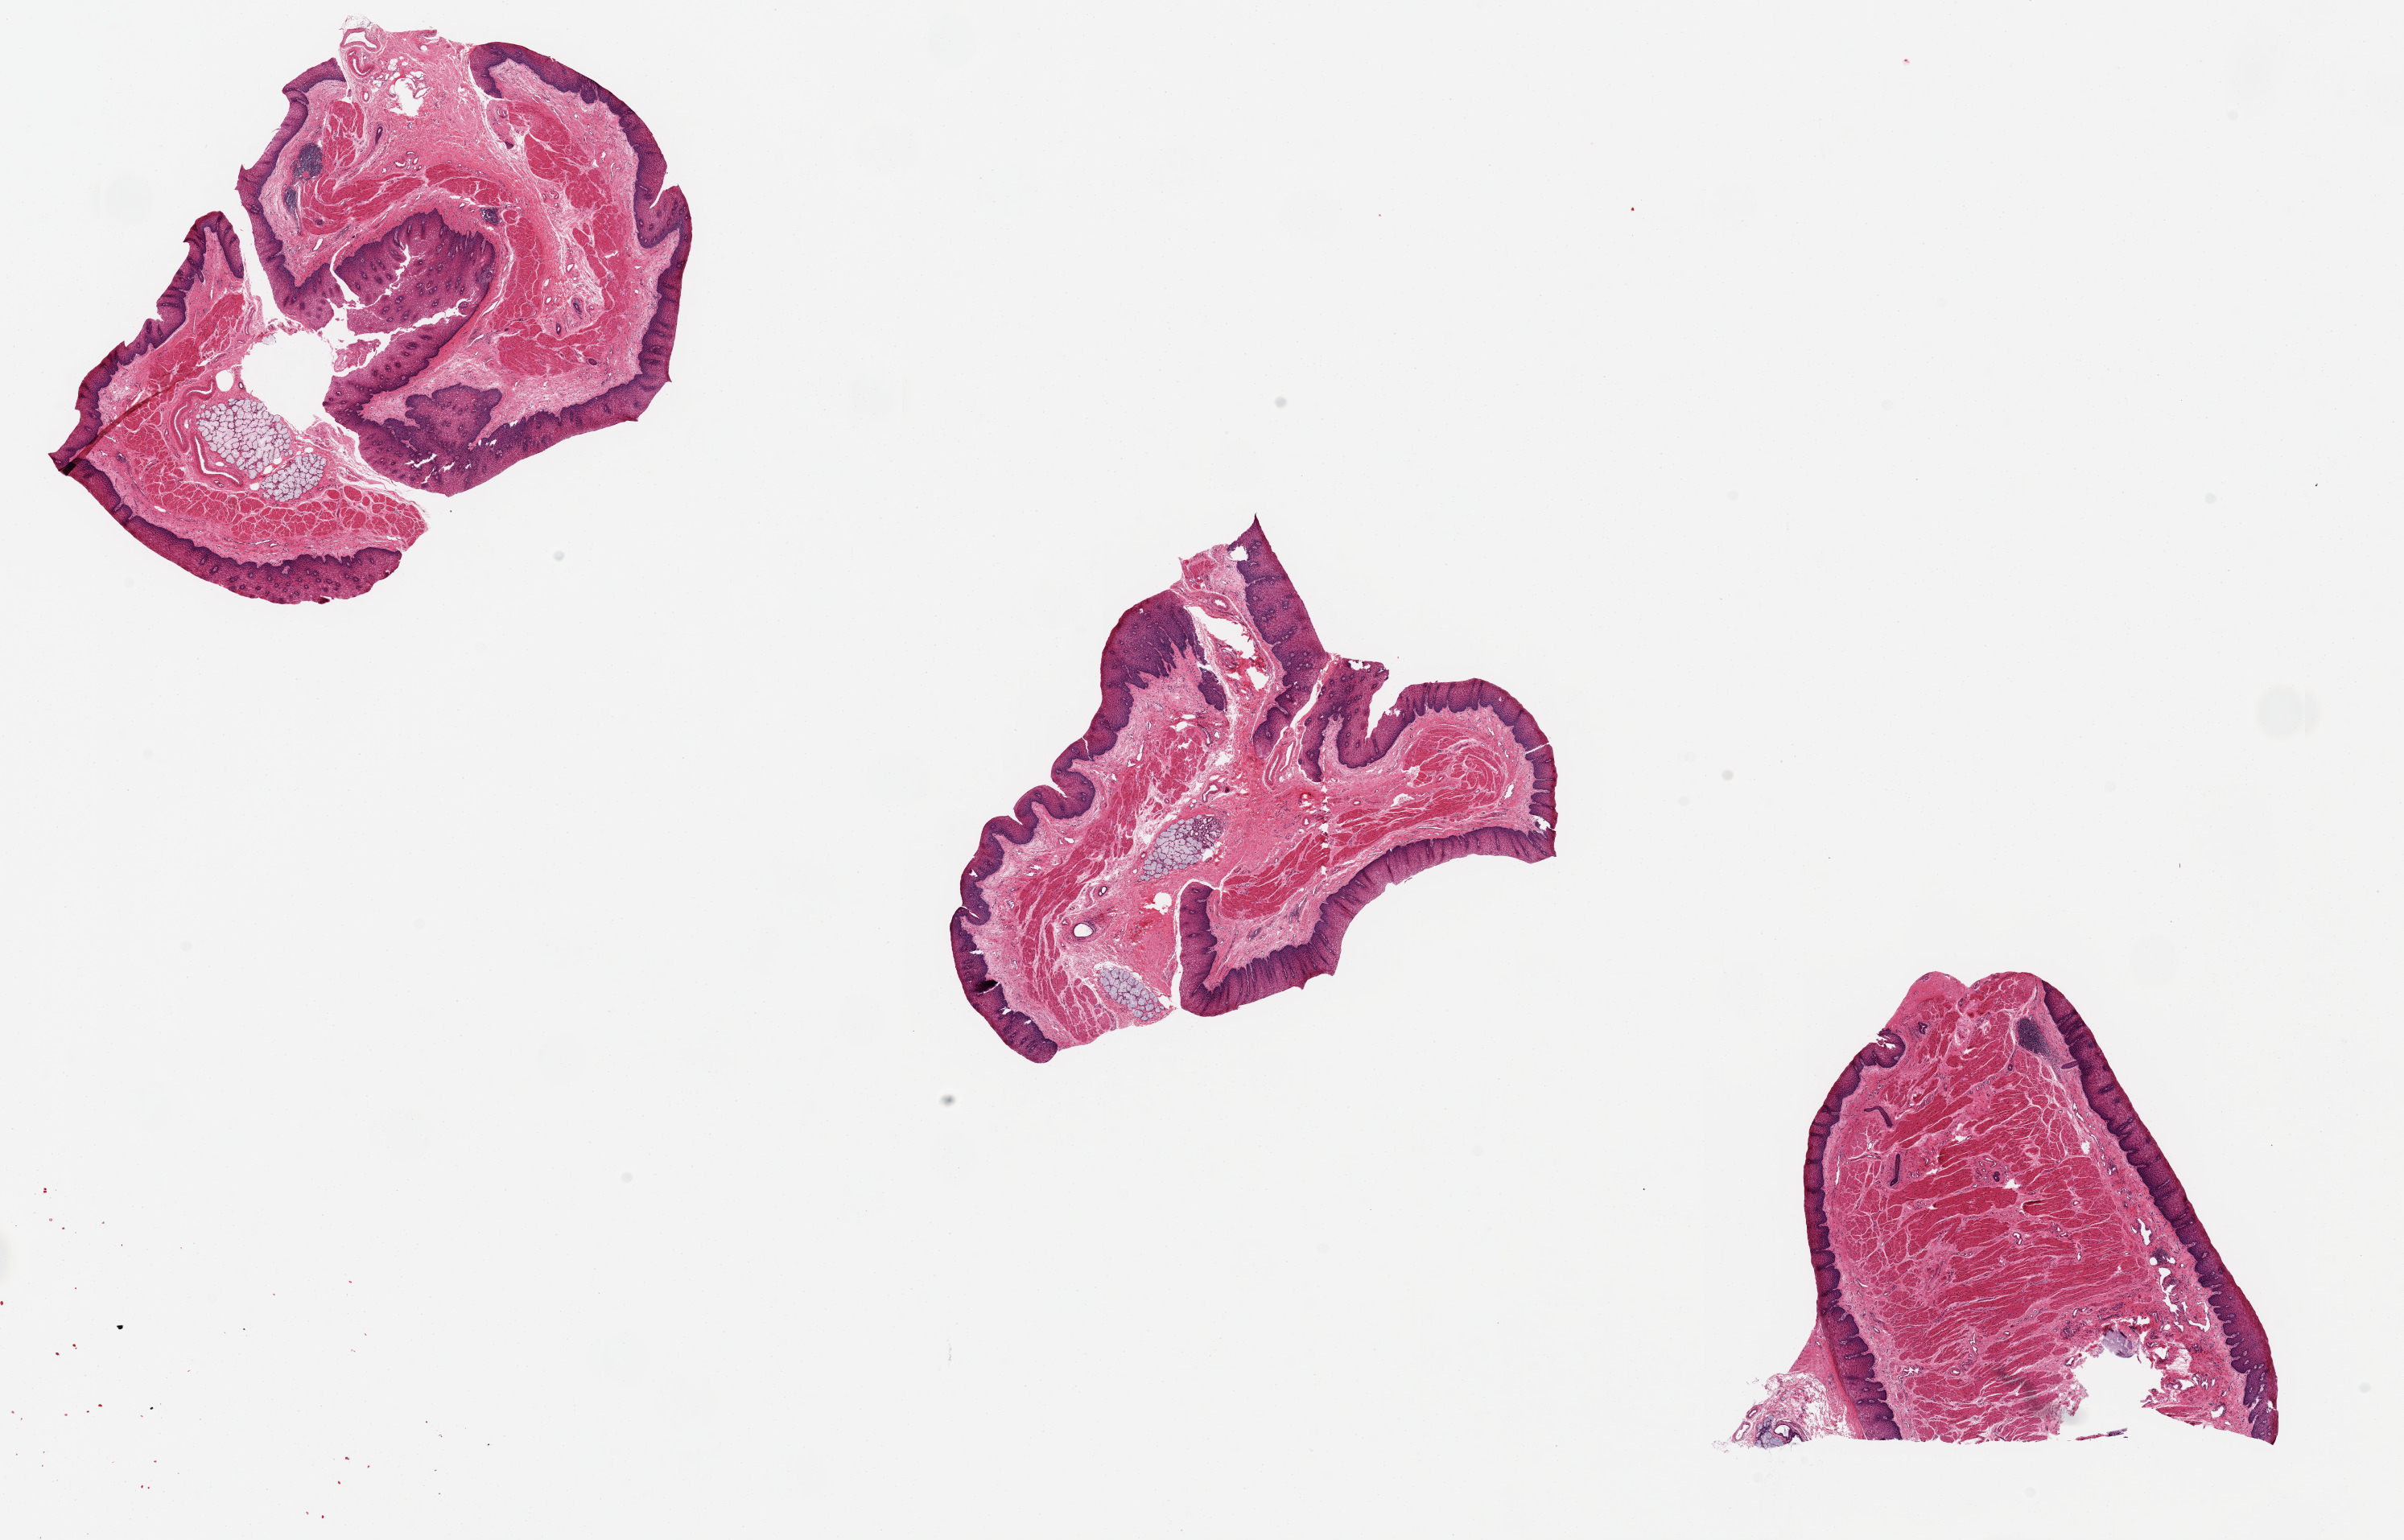
Digitized hematoxylin and eosin (H&E)-stained section, low-resolution overview of the scanned area, about 23.6 x 15.1 mm; PAXgene-fixed, paraffin-embedded tissue; target tissue: esophageal mucous membrane; tissue donor sample. Male donor.
Reviewer comment on this tissue sample: 3 pieces up to 6.4x4.6 mm; 1 has prominent muscularis mucosae.